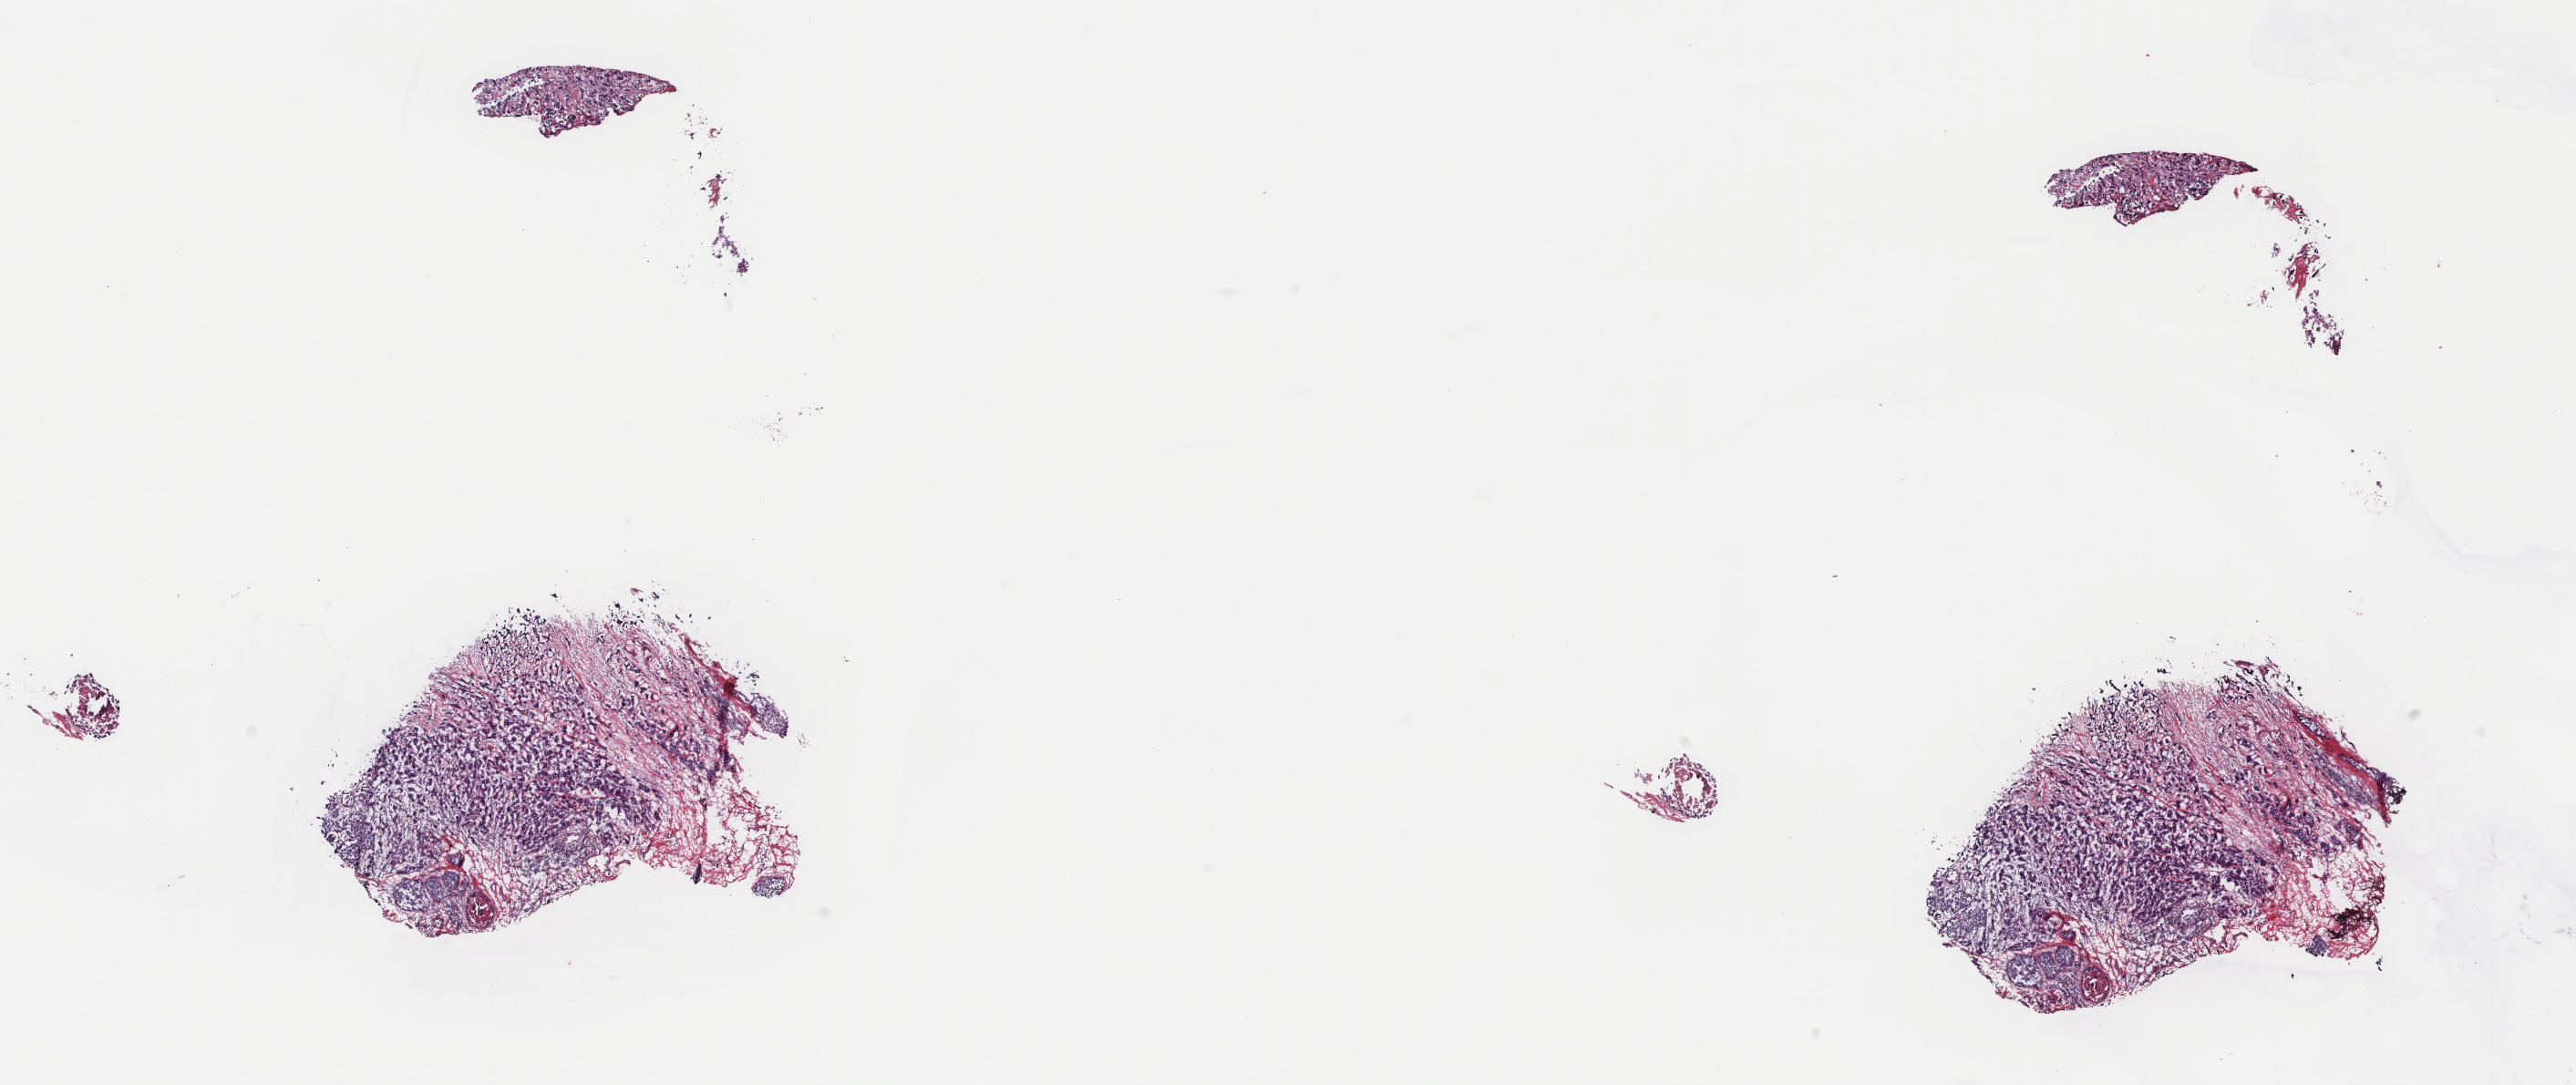
Hematoxylin and eosin (H&E) stained whole-slide image, whole scanned area (about 22.4 x 9.4 mm, from a 40x scan) shown as a low-resolution overview. Frozen section. Sample: primary tumour, breast. Patient: female, age at initial diagnosis 62 years. Pathologist review of this section (percent, as recorded): tumour cells 85%, tumour nuclei 68%, normal cells 0%, stromal cells 13%, necrosis 2%. Infiltration values recorded for this section: lymphocyte infiltration 0%, monocyte infiltration 0%, neutrophil infiltration 0%.
Diagnosis: Infiltrating duct carcinoma, NOS. AJCC pathologic stage: IIIA (6th edition).